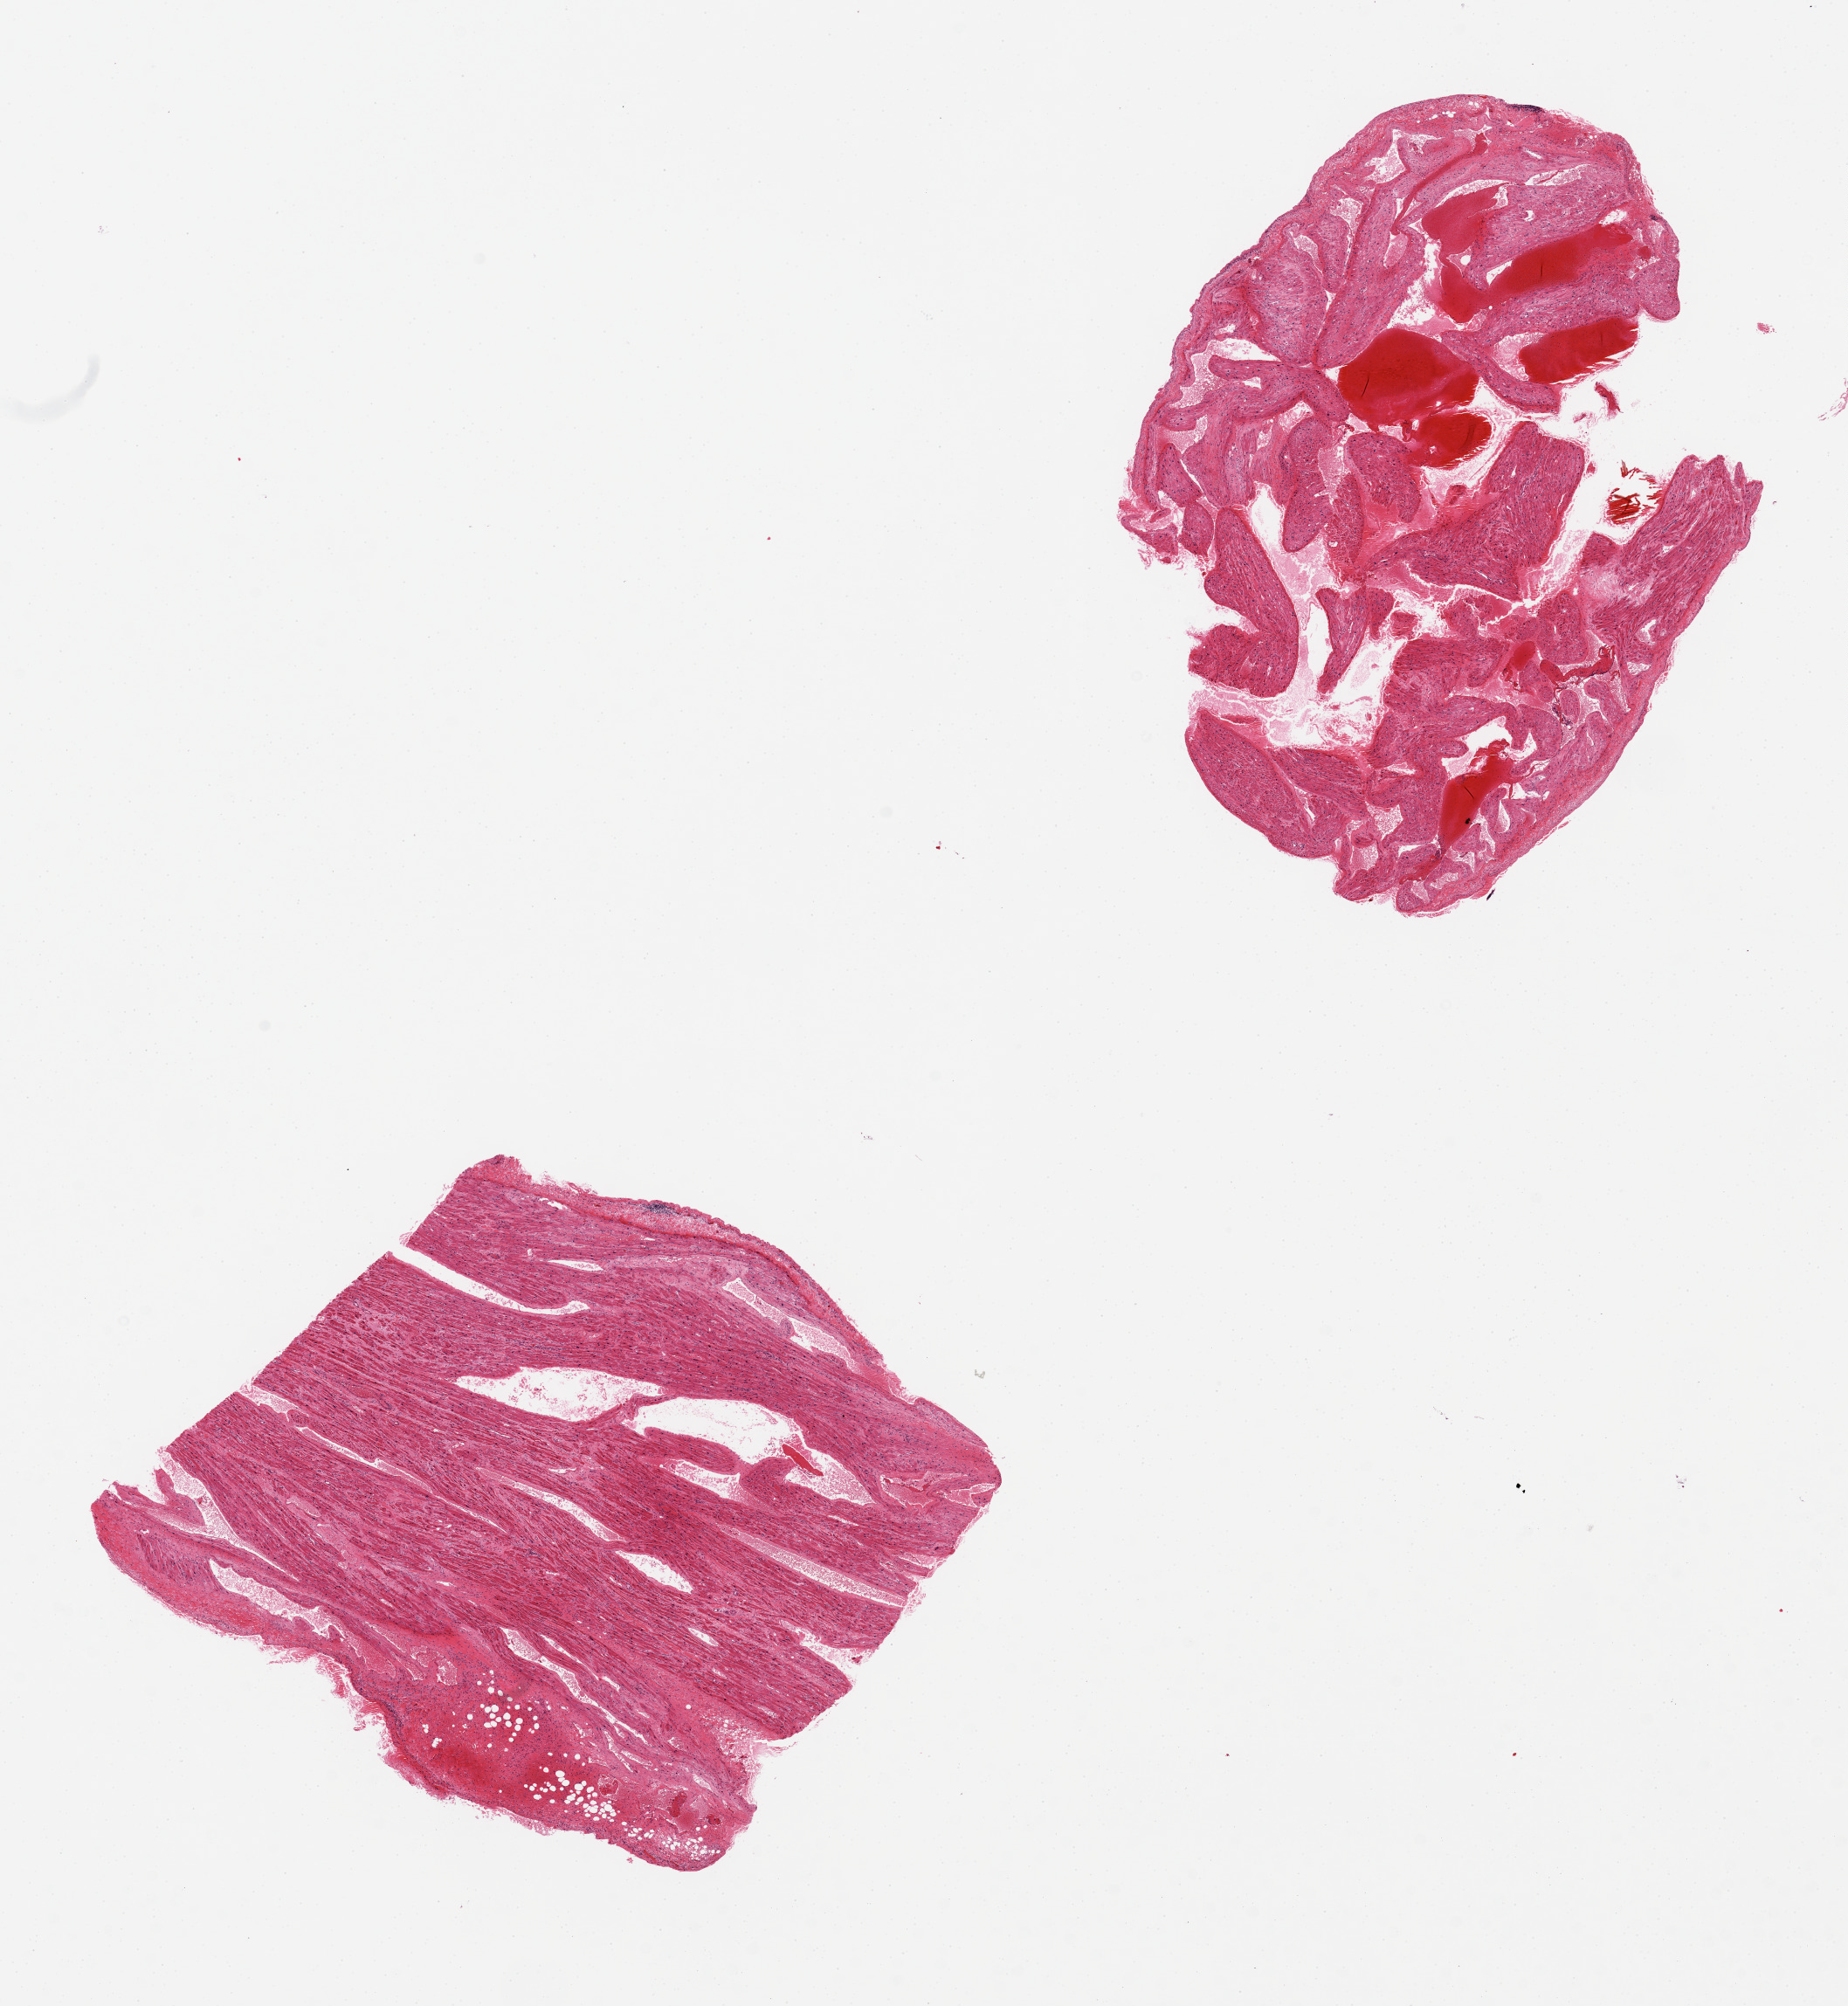
Hematoxylin and eosin (H&E) whole-slide image — a low-resolution overview of the entire scanned area, about 16.7 x 18.2 mm (slide scanned at 20x); PAXgene-fixed, paraffin-embedded tissue; section of auricular appendage (target tissue); tissue donor sample. Female donor.
Review note (as recorded): 2 pieces, no abnormalities.